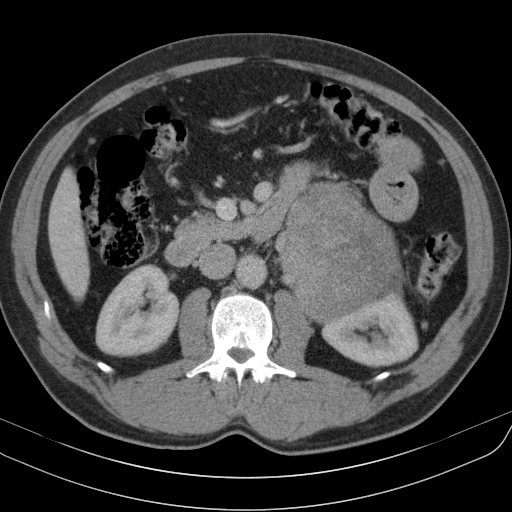
Contrast-enhanced abdominal CT, one axial slice. Intravenous contrast given. Soft-tissue window (W 400 / L 40 HU). 5 mm slice thickness. 512 × 512 image matrix, field of view 370 × 370 mm. Patient: male, 51 years. From the clinical record (not read from this slice): diagnosis: adrenocortical carcinoma; tumour side: left adrenal; tumour size at pathology: 18 cm; Ki-67 index: 40 %.
Annotated regions visible in this slice (semi-automatically segmented with operator editing):
- mass: bounding box (x1, y1, x2, y2) in pixels: (284, 189, 400, 321)